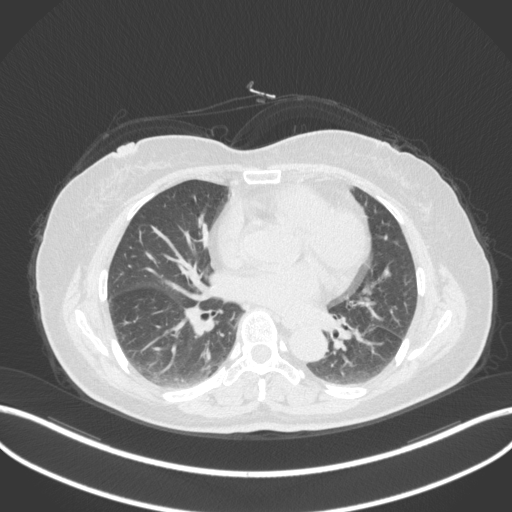
Chest CT, one axial slice. Lung window (W 1500 / L -600 HU). 512 × 512 image matrix, field of view 400 × 400 mm. Patient: female, 59 years. From the clinical record (not read from this slice): clinical TNM (as recorded): T2a N0 M0; histopathological grade: G2-3.
Outlined on this slice (rectangle marked by the reading radiologist):
- lung tumour (recorded histology: adenocarcinoma): bounding box [x1, y1, x2, y2] px = [355, 324, 381, 353]